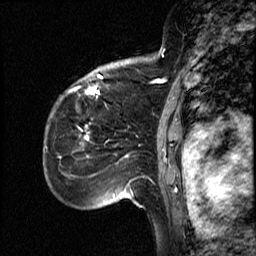
Breast MRI (dynamic contrast-enhanced), one sagittal slice; slice 38 of 50 in the series (ordered by position); dynamic contrast-enhanced study with each time point stored as its own series, time point 2 of 4 at this slice position (early post-contrast, ordered by acquisition time); 1.5 T; TE 4.2 ms, TR 18.5 ms; 3 mm slice thickness; 256 × 256 image matrix. Female patient, age 44 years. From the clinical record (not read from this slice): setting: breast cancer imaged before/during neoadjuvant chemotherapy; receptor status: HR-positive, HER2-negative.
Annotated regions visible in this slice (semi-automatic segmentation, software-assisted and operator-edited):
- analysis volume of interest (the breast-tissue region the enhancement analysis was run in; not a lesion): bounding box [x1, y1, x2, y2] px = [59, 85, 114, 206]
- tumour enhancement mask (voxels above the 100 % enhancement threshold inside the analysis volume of interest): [84, 134, 88, 140]